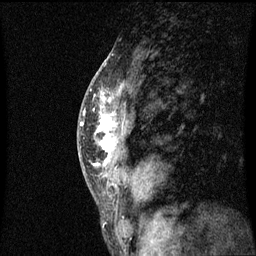
Breast MRI (dynamic contrast-enhanced), one sagittal slice. Position 36 of 60 along the scan axis. Dynamic contrast-enhanced series, image 2 of 3 at this slice position (ordered by acquisition). 1.5 T. TE 4.2 ms, TR 8.9 ms. 2 mm slice thickness. 256 × 256 image matrix. Patient: female, 50 years. From the clinical record (not read from this slice): setting: breast cancer imaged before/during neoadjuvant chemotherapy; receptor status: triple-negative.
Outlined on this slice (semi-automatic segmentation, software-assisted and operator-edited):
- analysis volume of interest (the breast-tissue region the enhancement analysis was run in; not a lesion): bounding box [x1, y1, x2, y2] px = [84, 80, 133, 171]
- tumour enhancement mask (voxels above the 70 % enhancement threshold inside the analysis volume of interest): [94, 92, 119, 167]